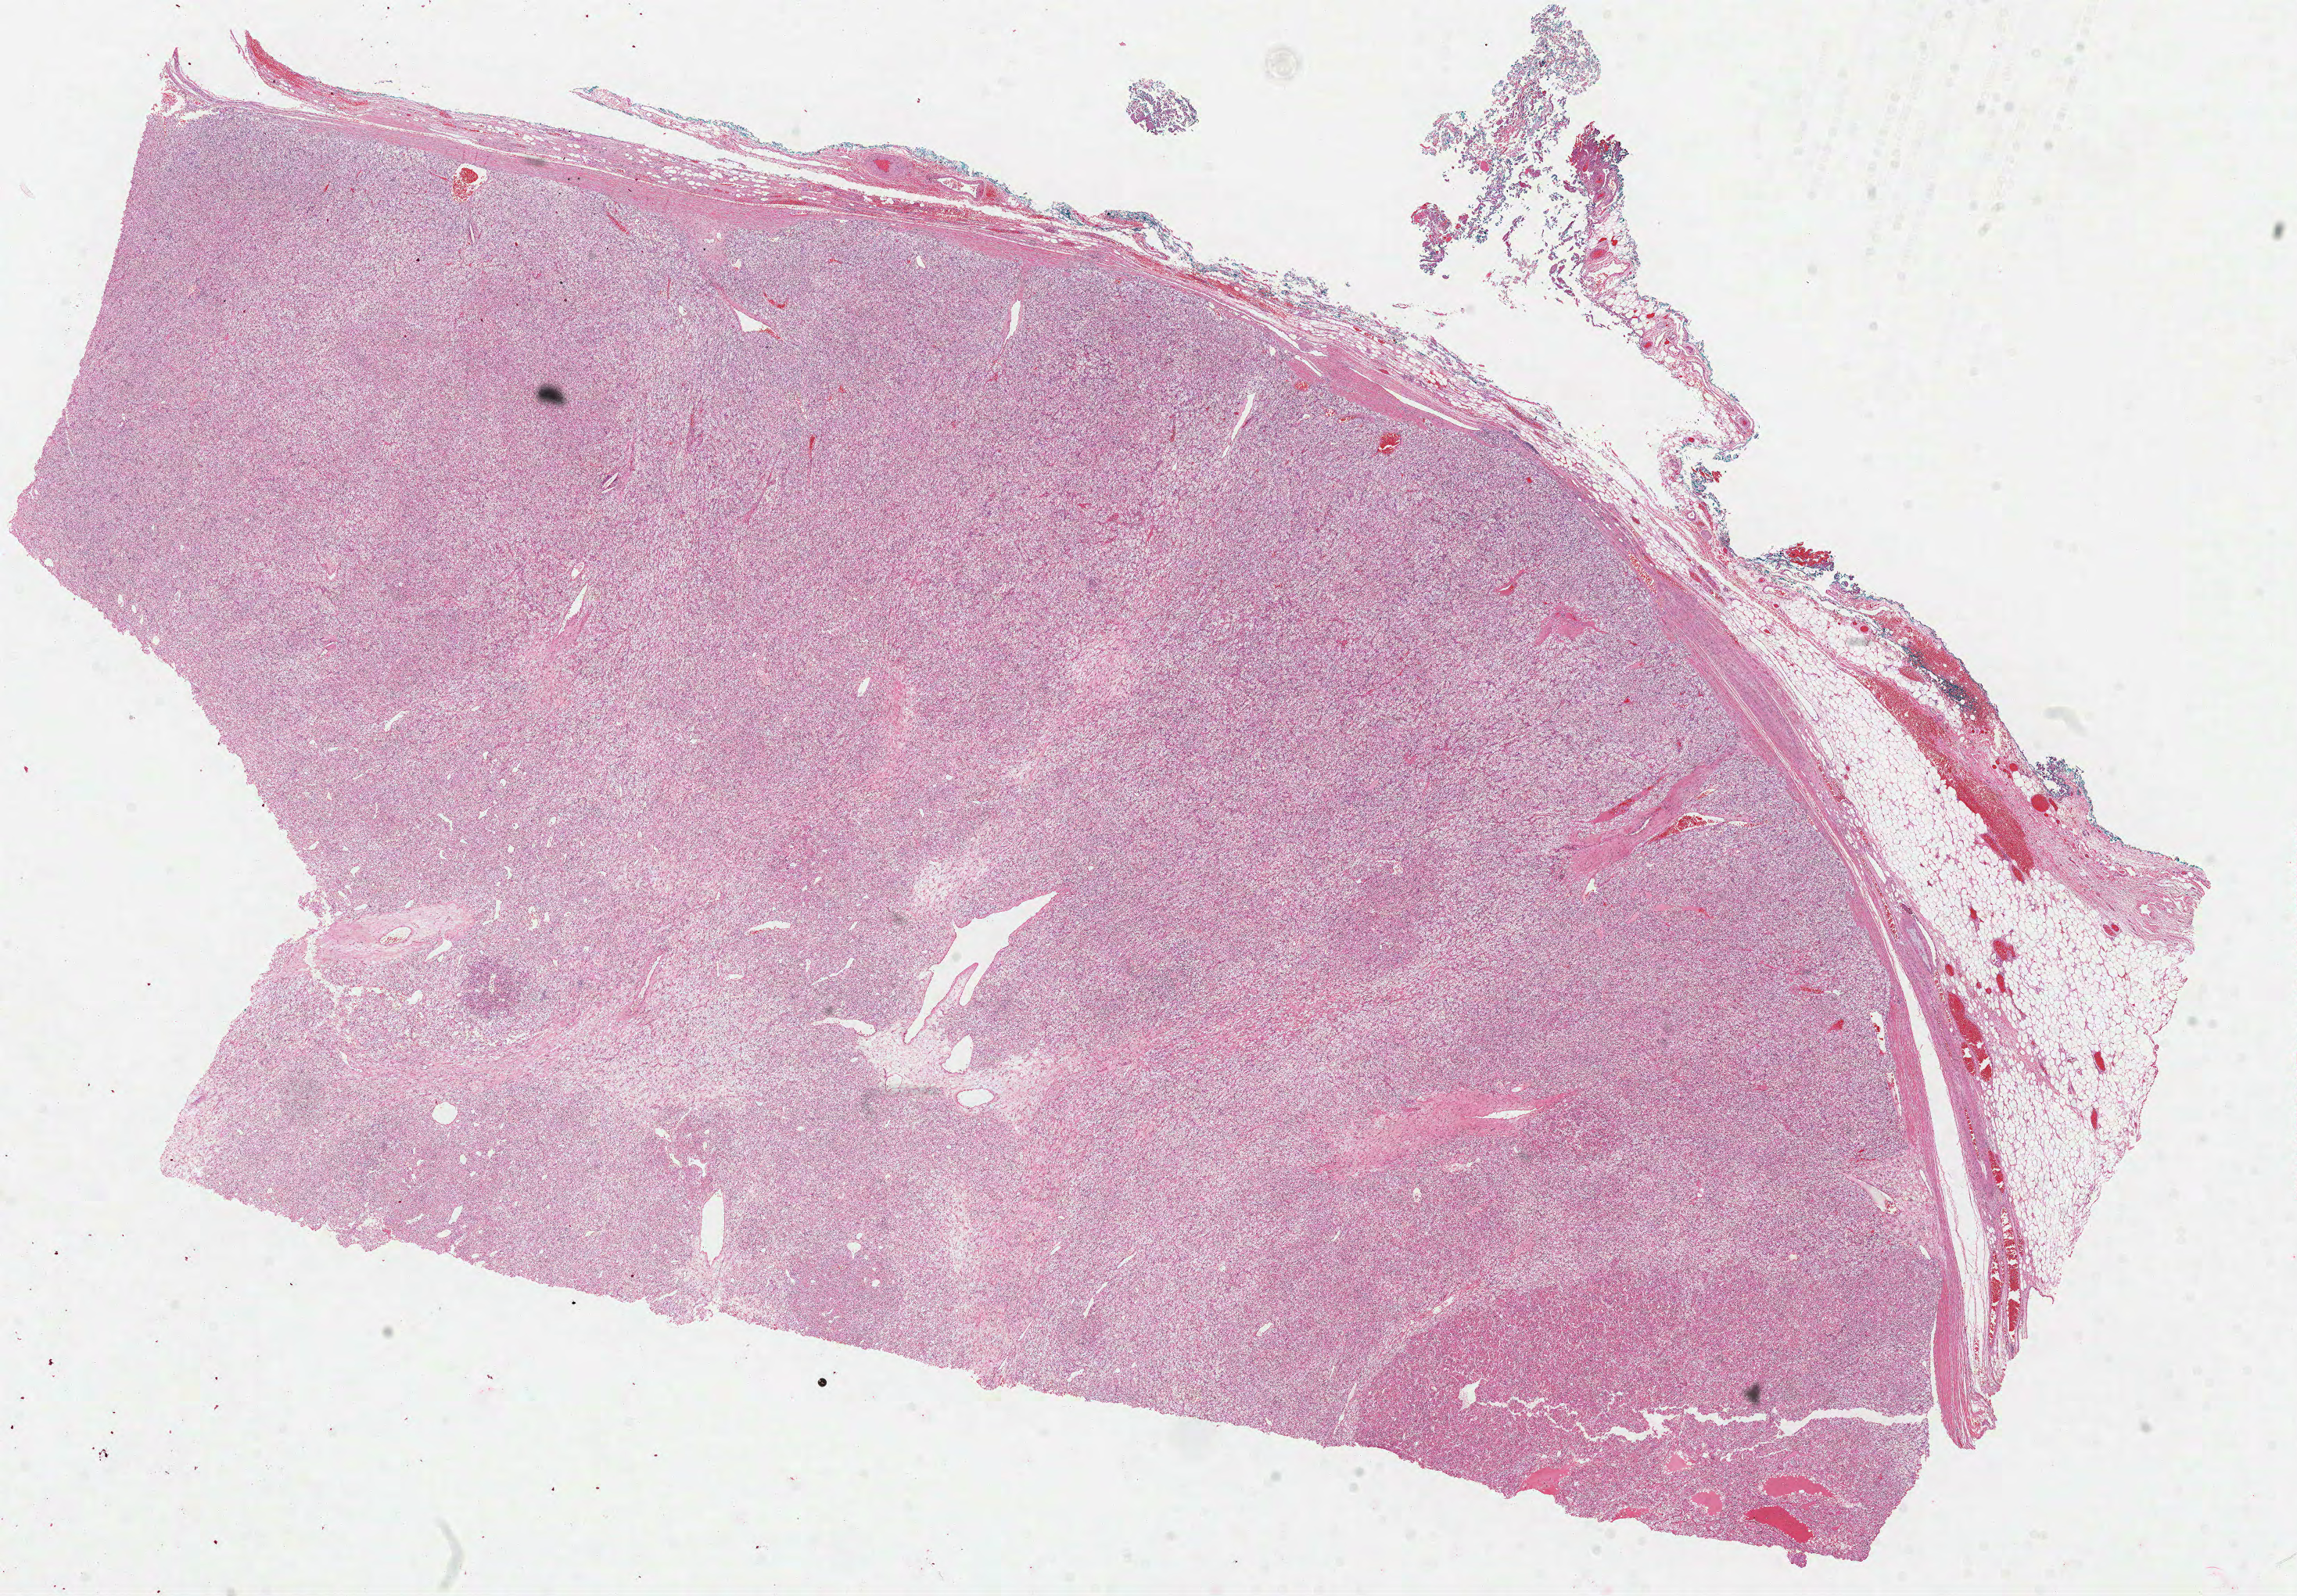
Whole-slide histology image, H&E-stained, low-resolution overview of the scanned area, about 23.7 x 16.5 mm; formalin-fixed paraffin-embedded (FFPE) diagnostic section; kidney, primary tumour sample. Male patient; age at initial diagnosis 79 years. Histologic grade: G3 (poorly differentiated).
AJCC pathologic stage: IV. TNM: T2 NX M1. Laterality: left. Diagnosis: Clear cell adenocarcinoma, NOS.